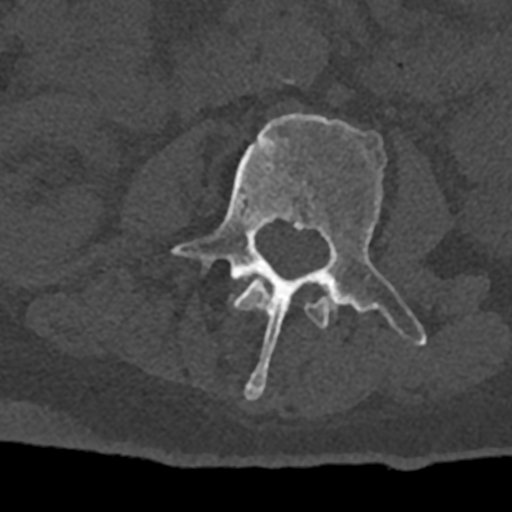
CT including the spine, one axial slice; position 325 of 797 along the scan axis; 120 kVp; bone window (W 1800 / L 400 HU); 0.5 mm slice thickness; 512 × 512 image matrix. Male patient, age 74 years. From the clinical record (not read from this slice): primary cancer: renal.
Structures marked on this image (semi-automatically segmented with operator editing):
- L2 vertebra: bounding box <231,280,329,329> (left, top, right, bottom; pixels)
- L3 vertebra: <169,113,427,399>